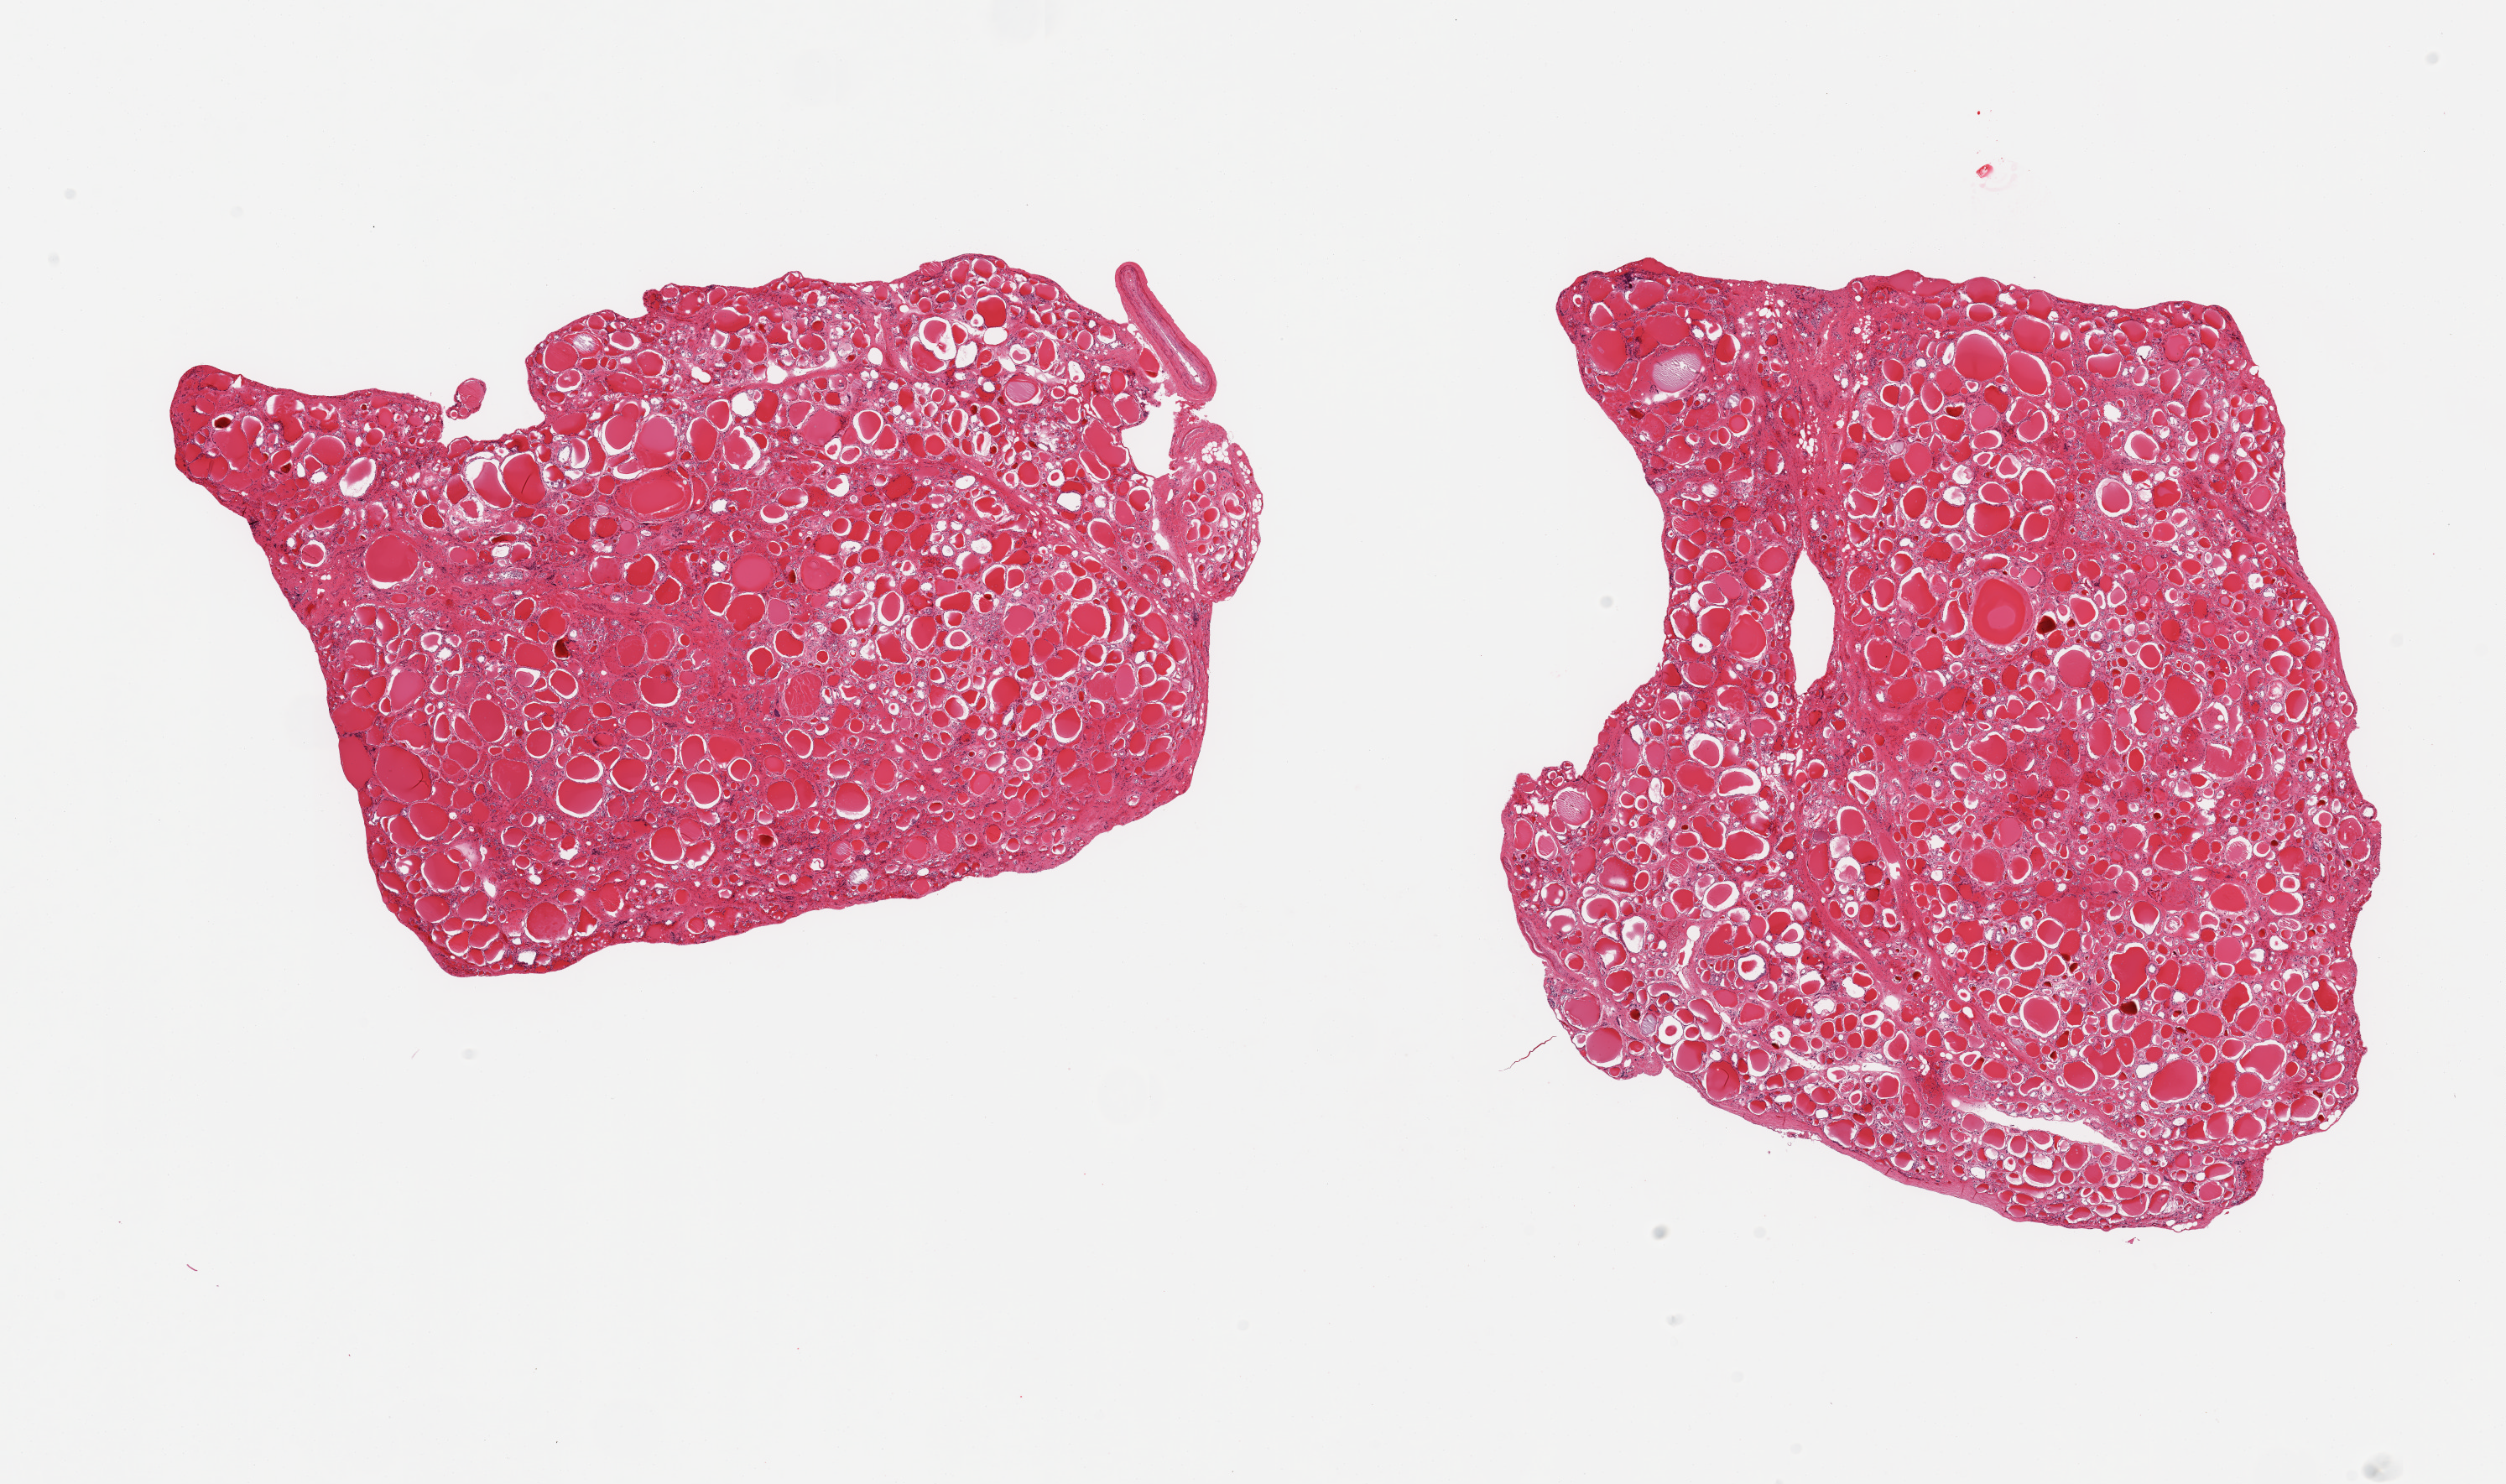
Hematoxylin and eosin (H&E) whole-slide image, brightfield, a low-resolution overview of the entire scanned area, about 23.6 x 14.0 mm (from a 20x scan); PAXgene-fixed, paraffin-embedded tissue; section of thyroid (target tissue); donor tissue sample. Donor sex: female.
Review note (as recorded): 2 pieces; mild interstitial fibrosis.